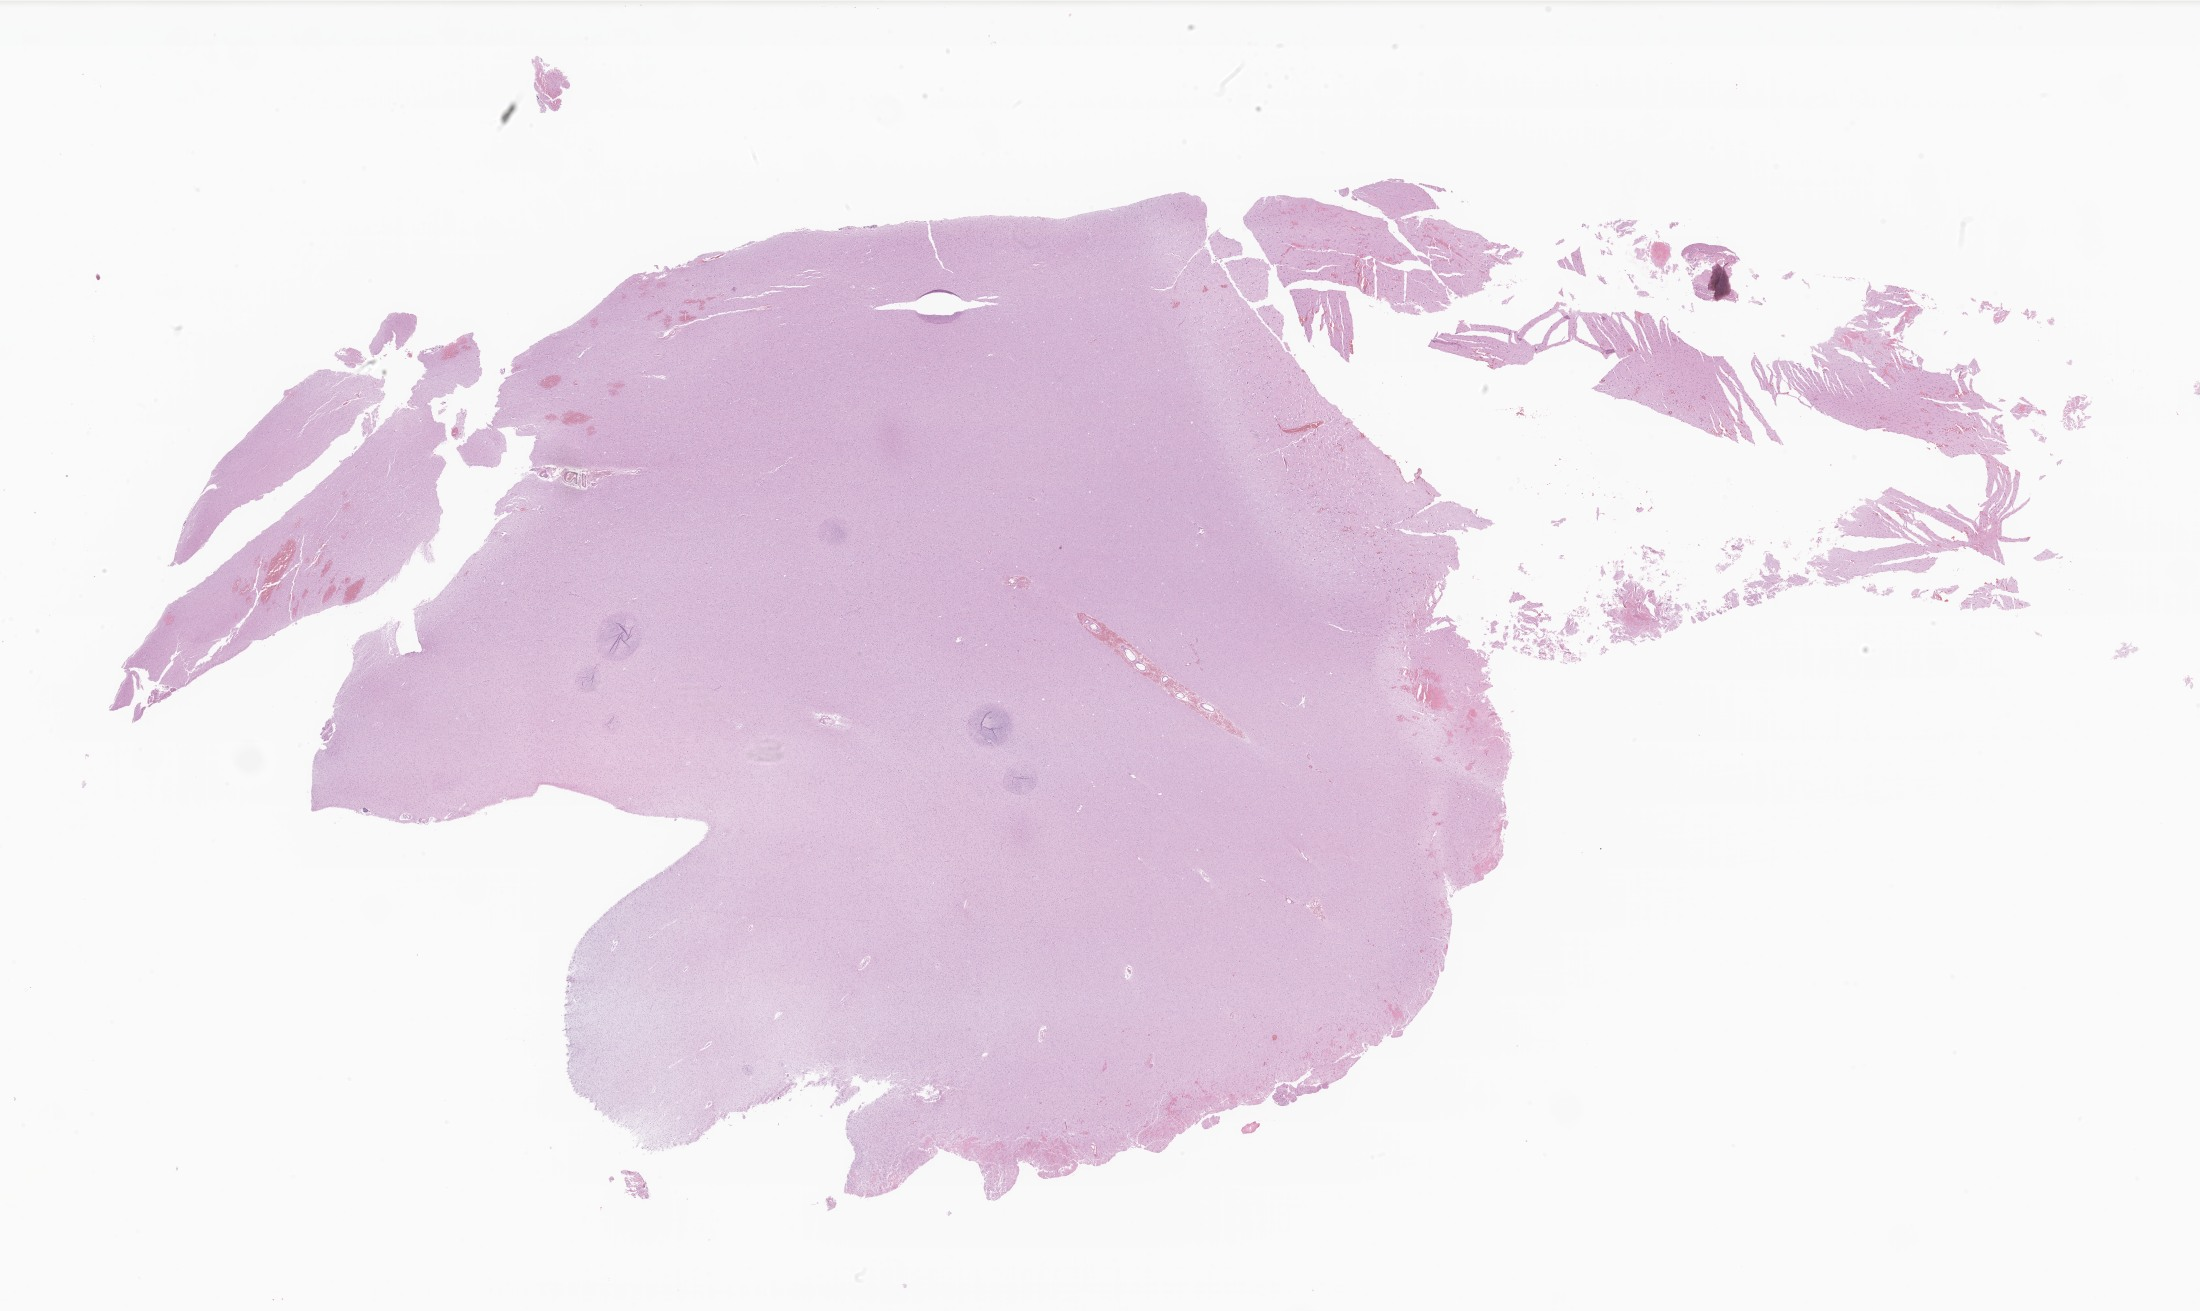
Digitized hematoxylin and eosin (H&E)-stained section of tumor tissue from the brain — a low-resolution overview of the entire scanned area, about 37.1 x 22.1 mm; FFPE section. Female patient, age 203 months (16 years 11 months).
* diagnosis (ICD-O-3 morphology term): Astrocytoma, anaplastic, NOS